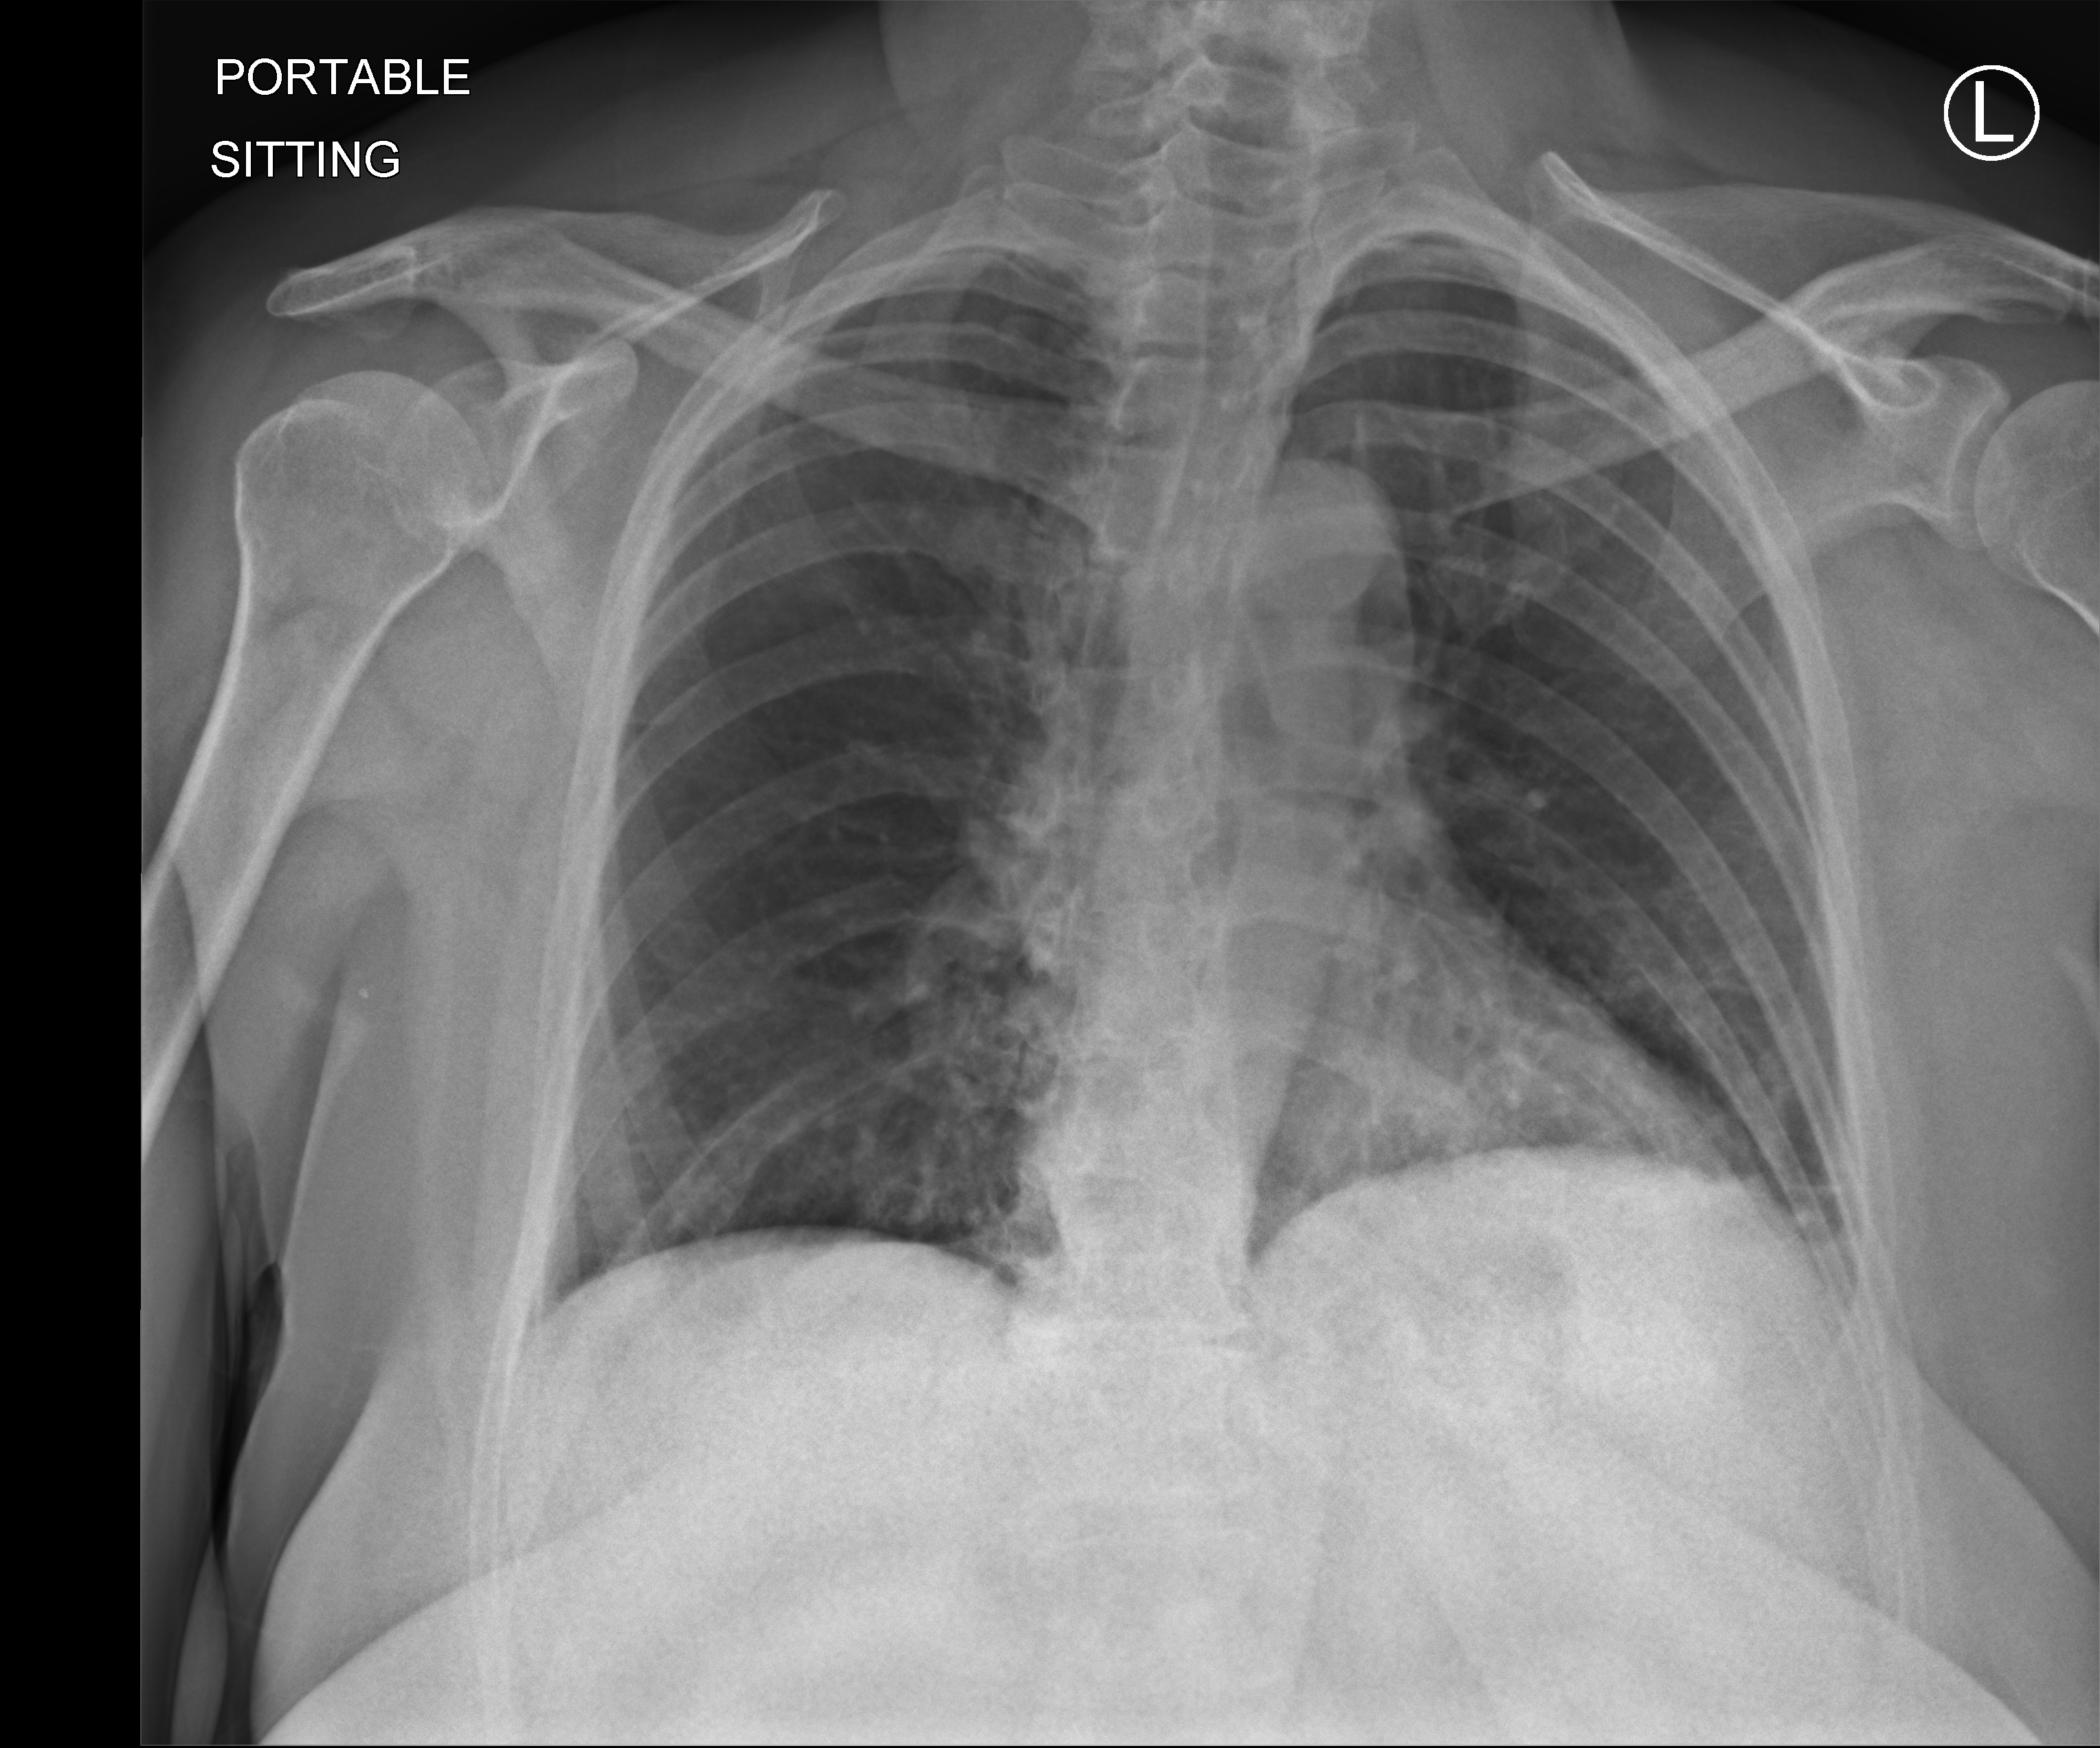
Portable chest radiograph; anteroposterior (AP) projection. Patient hospitalised with COVID-19; female, aged 18–59 years.
Admission-level facts for this patient (not findings on this image; timing relative to this image not recorded): diabetes (admission record): no; admitted to intensive care during this hospital stay: no; length of hospital stay: 8 days.